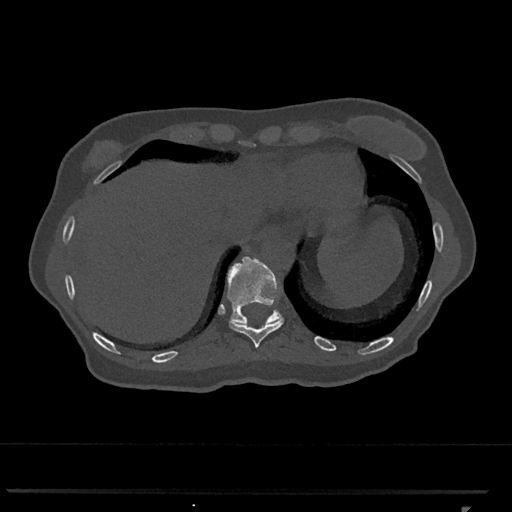
CT including the spine, one axial slice. Bone window (W 1800 / L 400 HU). 0.5 mm slice thickness. 512 × 512 image matrix, field of view 380 × 380 mm. Female patient, age 62 years. Case-level facts recorded for this patient, not image findings: primary cancer: renal.
Annotated regions visible in this slice (semi-automatic segmentation, software-assisted and operator-edited):
- T10 vertebra: box from (x=229, y=318) to (x=284, y=348) px
- T11 vertebra: (x=227, y=256)–(x=283, y=325)